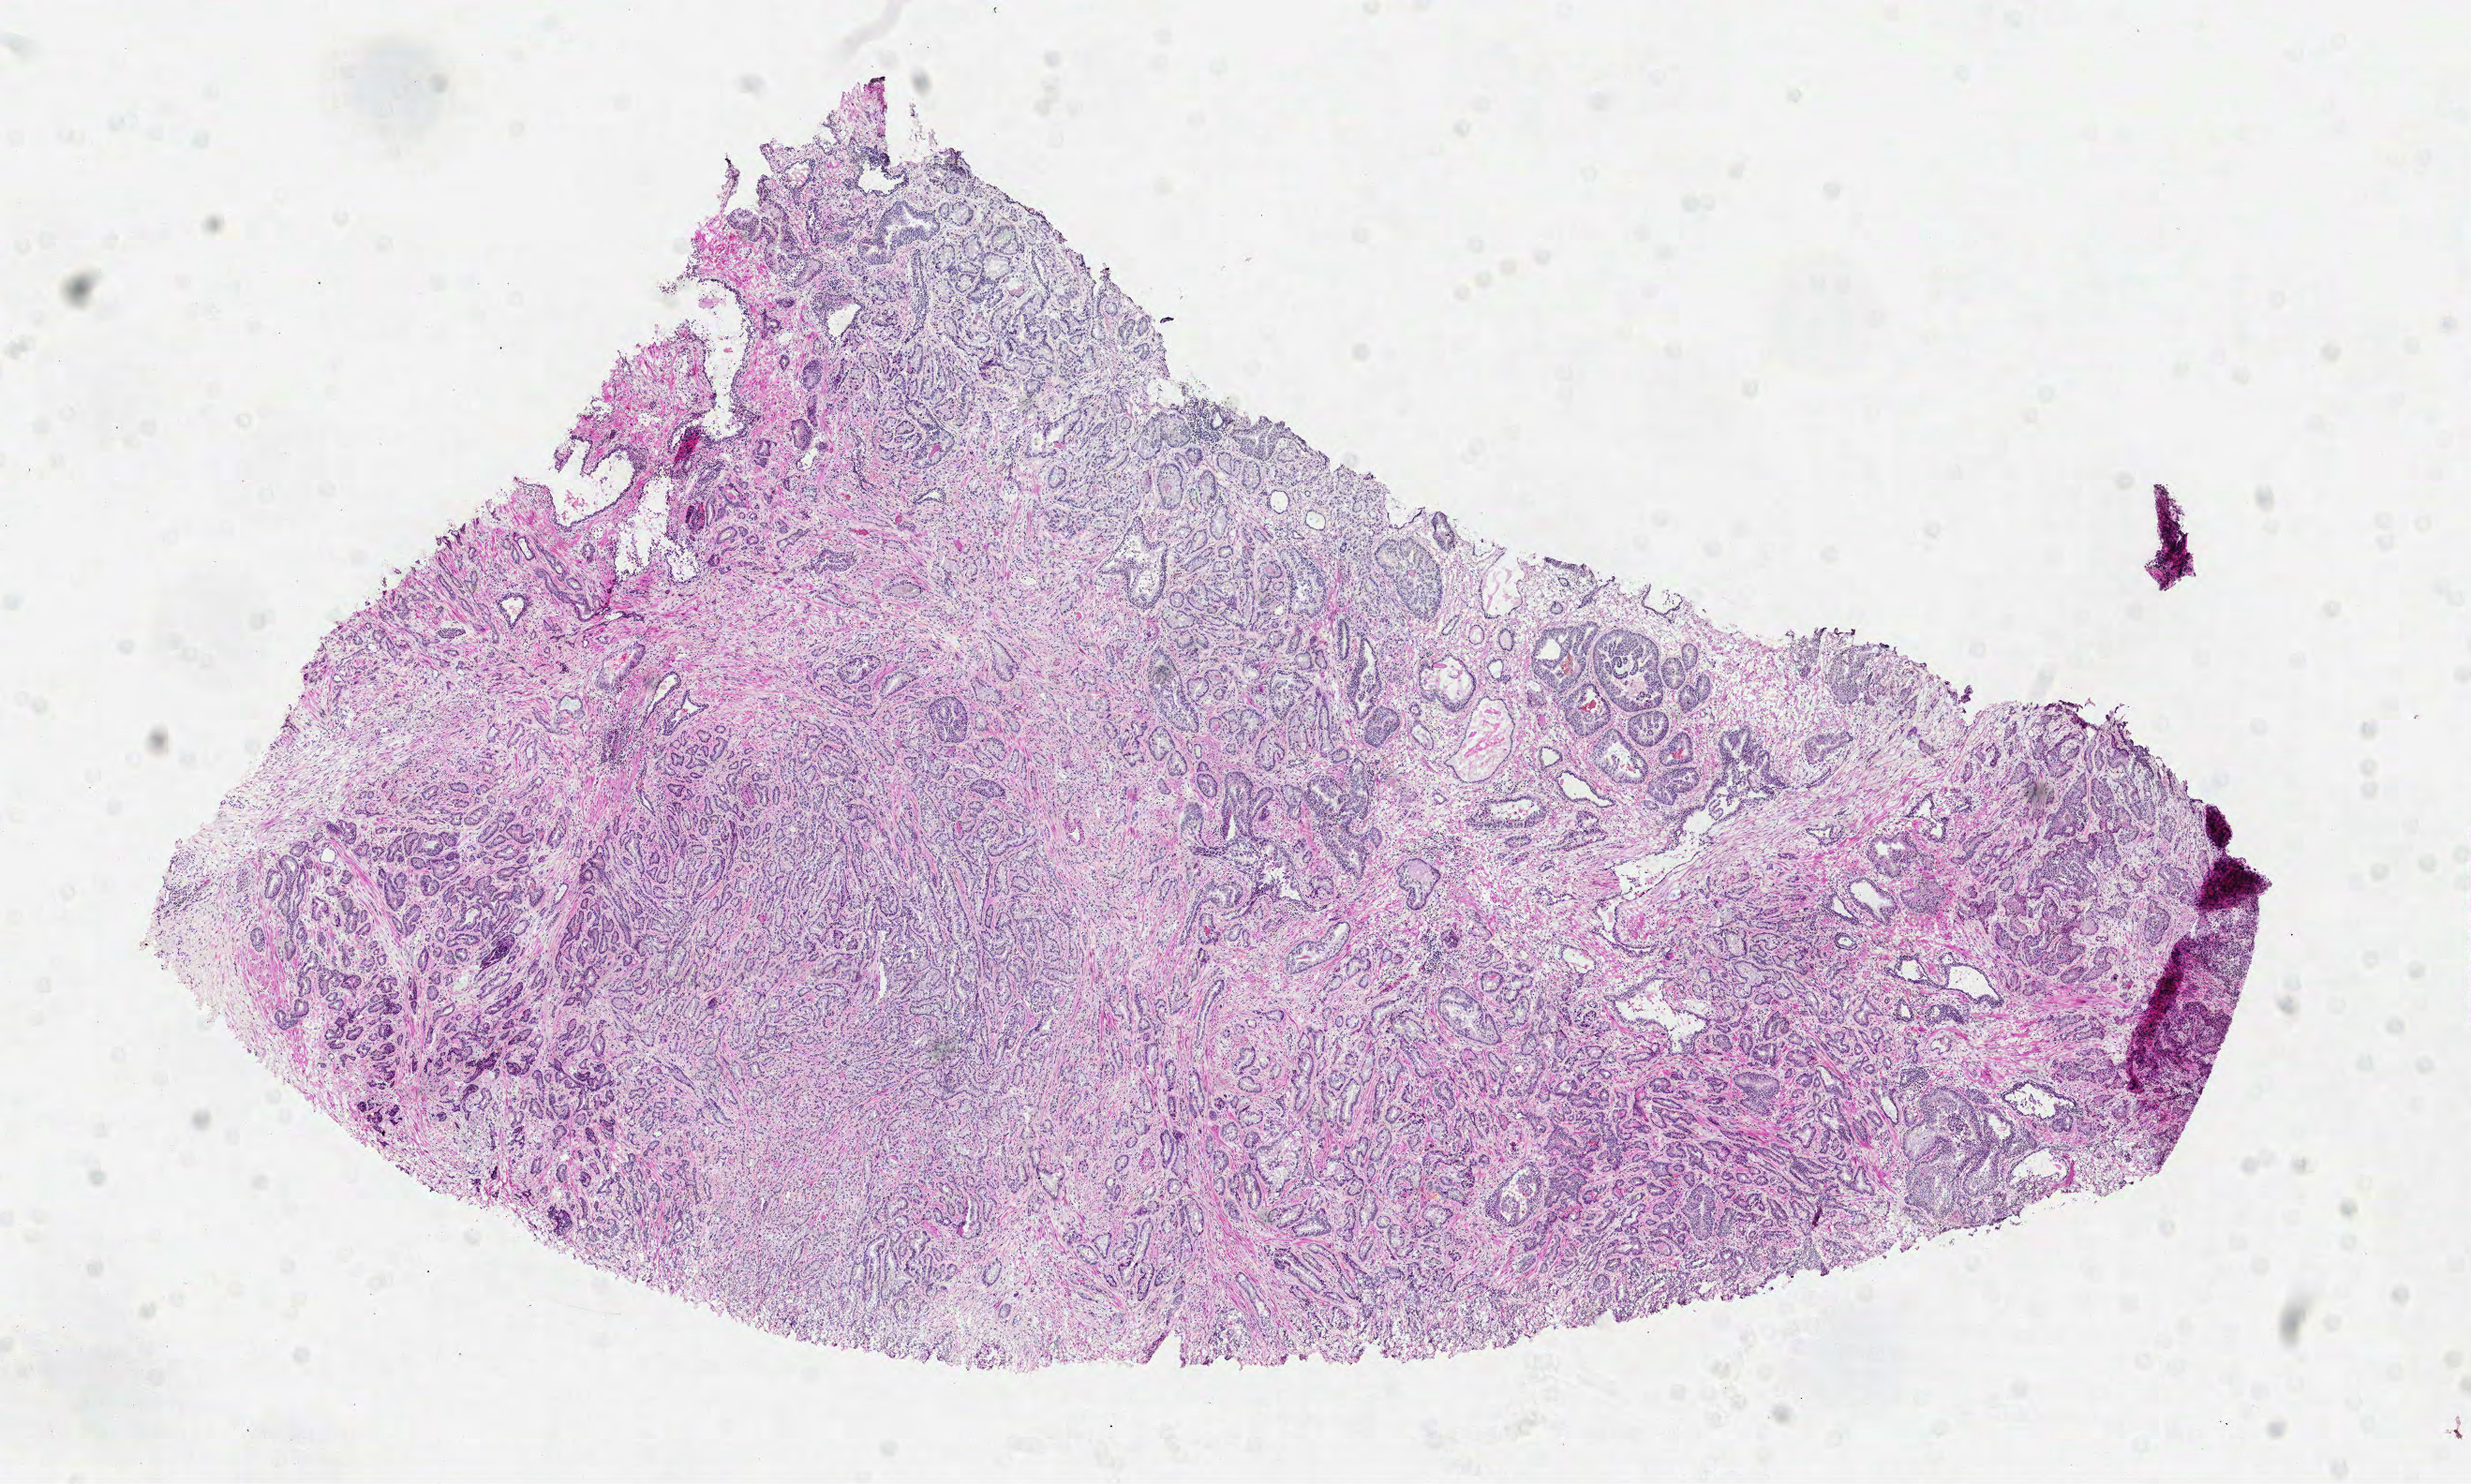
Whole-slide histology image, H&E-stained — low-resolution overview of the scanned area, about 10.6 x 6.4 mm. Formalin-fixed paraffin-embedded (FFPE) diagnostic section. Prostate, primary tumour sample. Male patient; age at initial diagnosis 61 years. Gleason score: 9 (5+4).
Diagnosis: Acinar cell carcinoma (prostate gland). Laterality: left. Lymph nodes positive (case pathology): 0 of 5 examined.